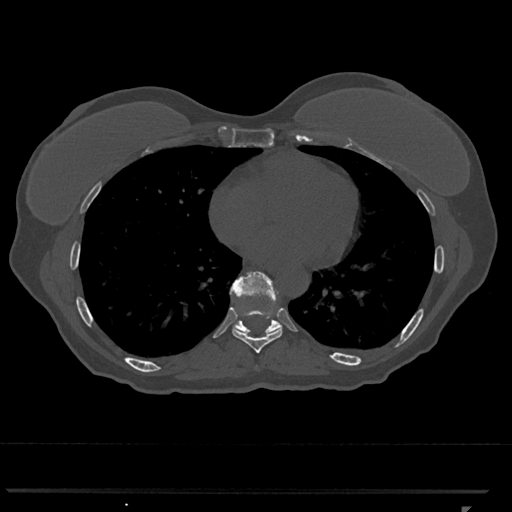
CT including the spine, one axial slice. Slice 650 of 793 in the series (ordered by position). Bone window (W 1800 / L 400 HU). 512 × 512 image matrix. Female patient, age 62 years. Case-level facts recorded for this patient, not image findings: primary cancer: renal.
Annotated regions visible in this slice (semi-automatic segmentation, software-assisted and operator-edited):
- T8 vertebra: bounding box (x1, y1, x2, y2) in pixels: (233, 309, 283, 354)
- T9 vertebra: (230, 272, 282, 335)